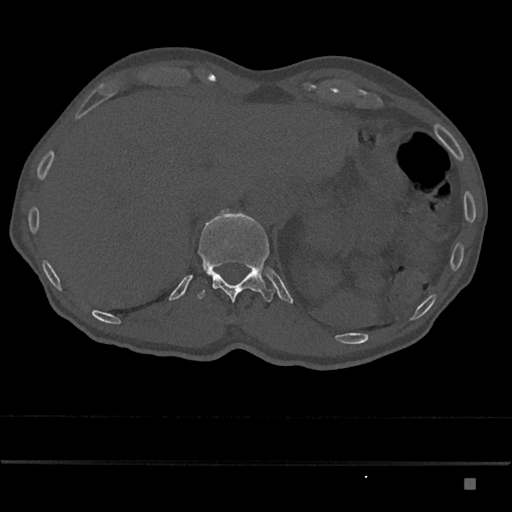
CT including the spine, one axial slice. Position 613 of 797 along the scan axis. Reconstruction kernel Br40s/3. 120 kVp. Bone window (W 1800 / L 400 HU). 0.5 mm slice thickness. 512 × 512 image matrix, field of view 390 × 390 mm. Patient: male, 72 years. Case-level facts recorded for this patient, not image findings: primary cancer: prostate.
Structures marked on this image (semi-automatically segmented with operator editing):
- T12 vertebra: bounding box <197,213,277,303> (left, top, right, bottom; pixels)